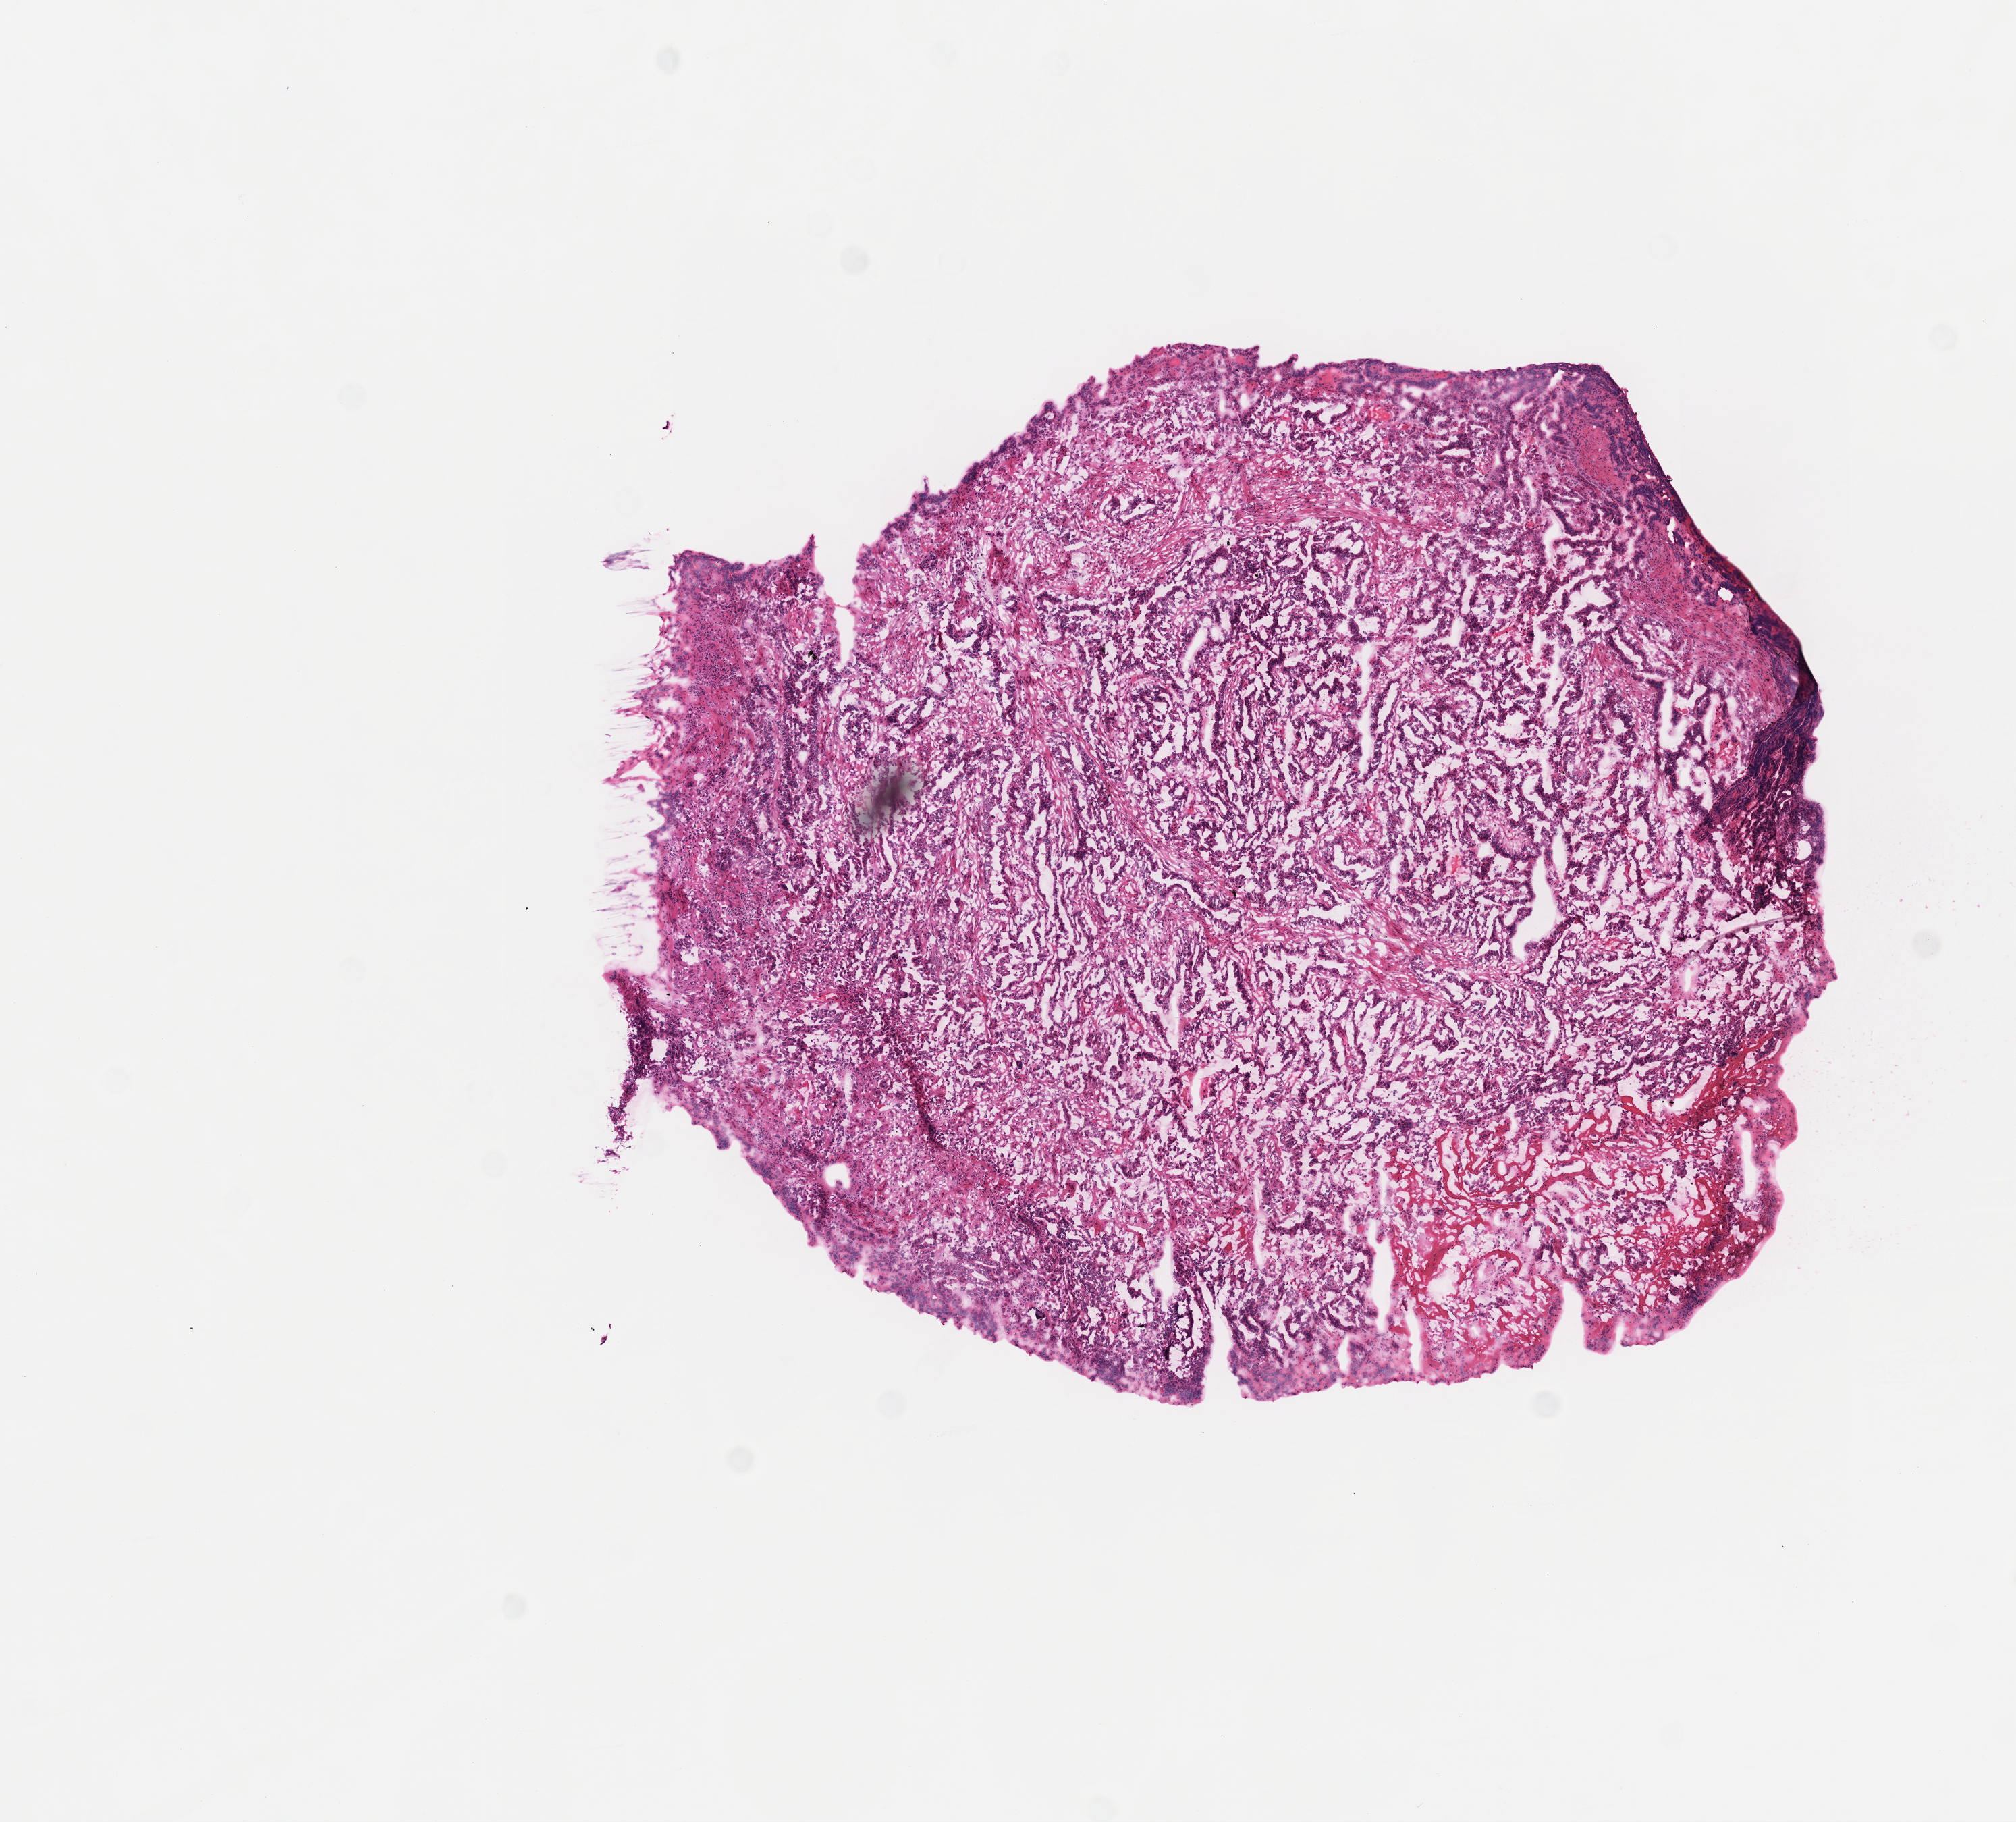
H&E-stained whole-slide image, shown as a low-resolution overview of the whole scanned area (about 6.0 x 5.5 mm, from a 40x scan), frozen section, stomach, primary tumour sample. Male patient; age at initial diagnosis 70 years. Histologic grade: G2 (moderately differentiated). Pathologist review of this section (percent, as recorded): tumour cells 100%, tumour nuclei 60%, normal cells 0%, stromal cells 0%, necrosis 0%. Inflammatory infiltration, as recorded: lymphocyte infiltration 3%, monocyte infiltration 0%, neutrophil infiltration 0%.
• pathologic diagnosis: Adenocarcinoma, NOS (lesser curvature of stomach, NOS)
• lymph nodes positive (case pathology): 0 of 15 examined
• AJCC pathologic stage: IB (6th edition)